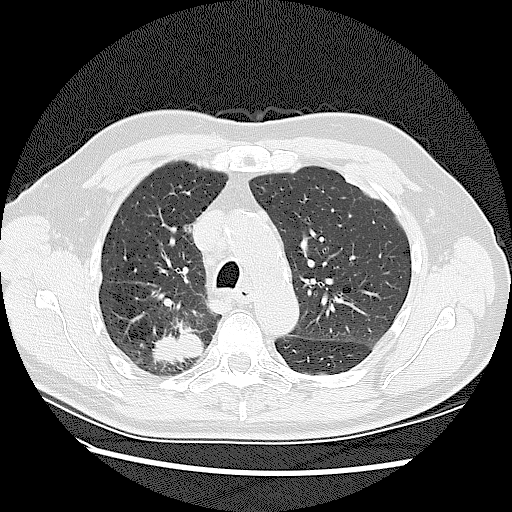
Low-dose screening chest CT, axial slice, baseline screening round, lung window (W 1500 / L -600 HU). Male, age 72 years at enrolment.
Expert reader's lesion annotation, box from (x=140, y=313) to (x=213, y=377) px. The screening reader recorded 2 non-calcified nodules or masses ≥4 mm on this exam (right upper lobe, right upper lobe); which of them this box marks is not recorded. Official screen result: positive, change unspecified: nodule(s) >= 4 mm or enlarging nodule(s), mass(es), or other non-specific abnormalities suspicious for lung cancer. Lung cancer was diagnosed 42 days after this screen: adenocarcinoma, NOS, right upper lobe, stage IV (AJCC 6th edition), 45 mm at pathology.